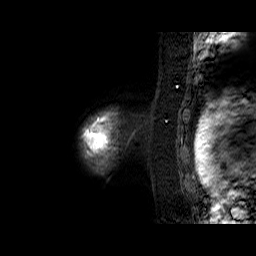
Breast MRI (dynamic contrast-enhanced), one sagittal slice. Position 56 of 60 along the scan axis. Dynamic contrast-enhanced series, time point 2 of 6 at this slice position (early post-contrast). 1.5 T. TE 6.3 ms, TR 32.9 ms. 4 mm slice thickness. 256 × 256 image matrix. Female patient. From the clinical record (not read from this slice): setting: breast cancer imaged before/during neoadjuvant chemotherapy; receptor status: triple-negative.
Outlined on this slice (semi-automatically segmented with operator editing):
- analysis volume of interest (the breast-tissue region the enhancement analysis was run in; not a lesion): bounding box [x1, y1, x2, y2] px = [82, 110, 118, 170]
- tumour enhancement mask (voxels above the 100 % enhancement threshold inside the analysis volume of interest): [82, 113, 117, 158]